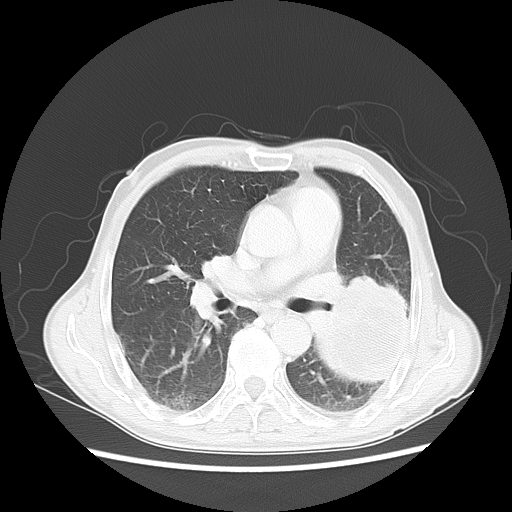
Chest CT, one axial slice. Position 28 of 51 along the scan axis. 120 kVp. Lung window (W 1500 / L -600 HU). 5 mm slice thickness. 512 × 512 image matrix. Male patient, age 64 years. From the clinical record (not read from this slice): clinical TNM (as recorded): T4 N0 M0.
Outlined on this slice (bounding box drawn by a radiologist):
- lung tumour (recorded histology: squamous cell carcinoma): bounding box (x1, y1, x2, y2) in pixels: (304, 266, 413, 380)